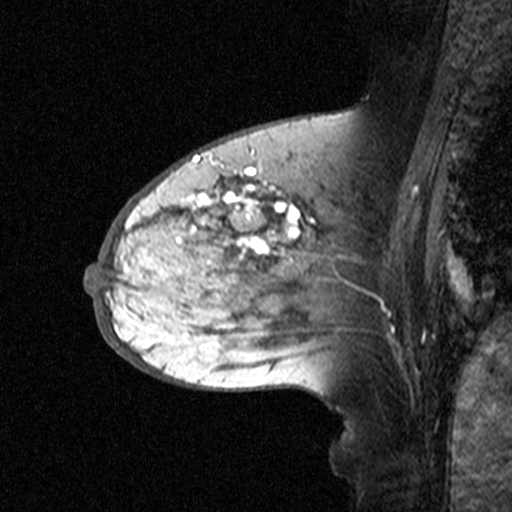
Breast MRI (dynamic contrast-enhanced), one sagittal slice; slice 22 of 44 in the series (ordered by position); dynamic contrast-enhanced study with each time point stored as its own series, time point 2 of 3 at this slice position (early post-contrast, ordered by acquisition time); 1.5 T; TE 4.5 ms, TR 11 ms; 512 × 512 image matrix. Female patient, age 65 years. From the clinical record (not read from this slice): setting: breast cancer imaged before/during neoadjuvant chemotherapy; receptor status: HER2-positive.
Annotated regions visible in this slice (semi-automatically segmented with operator editing):
- analysis volume of interest (the breast-tissue region the enhancement analysis was run in; not a lesion): bounding box <160,172,329,345> (left, top, right, bottom; pixels)
- tumour enhancement mask (voxels above the 90 % enhancement threshold inside the analysis volume of interest): <186,172,314,286>